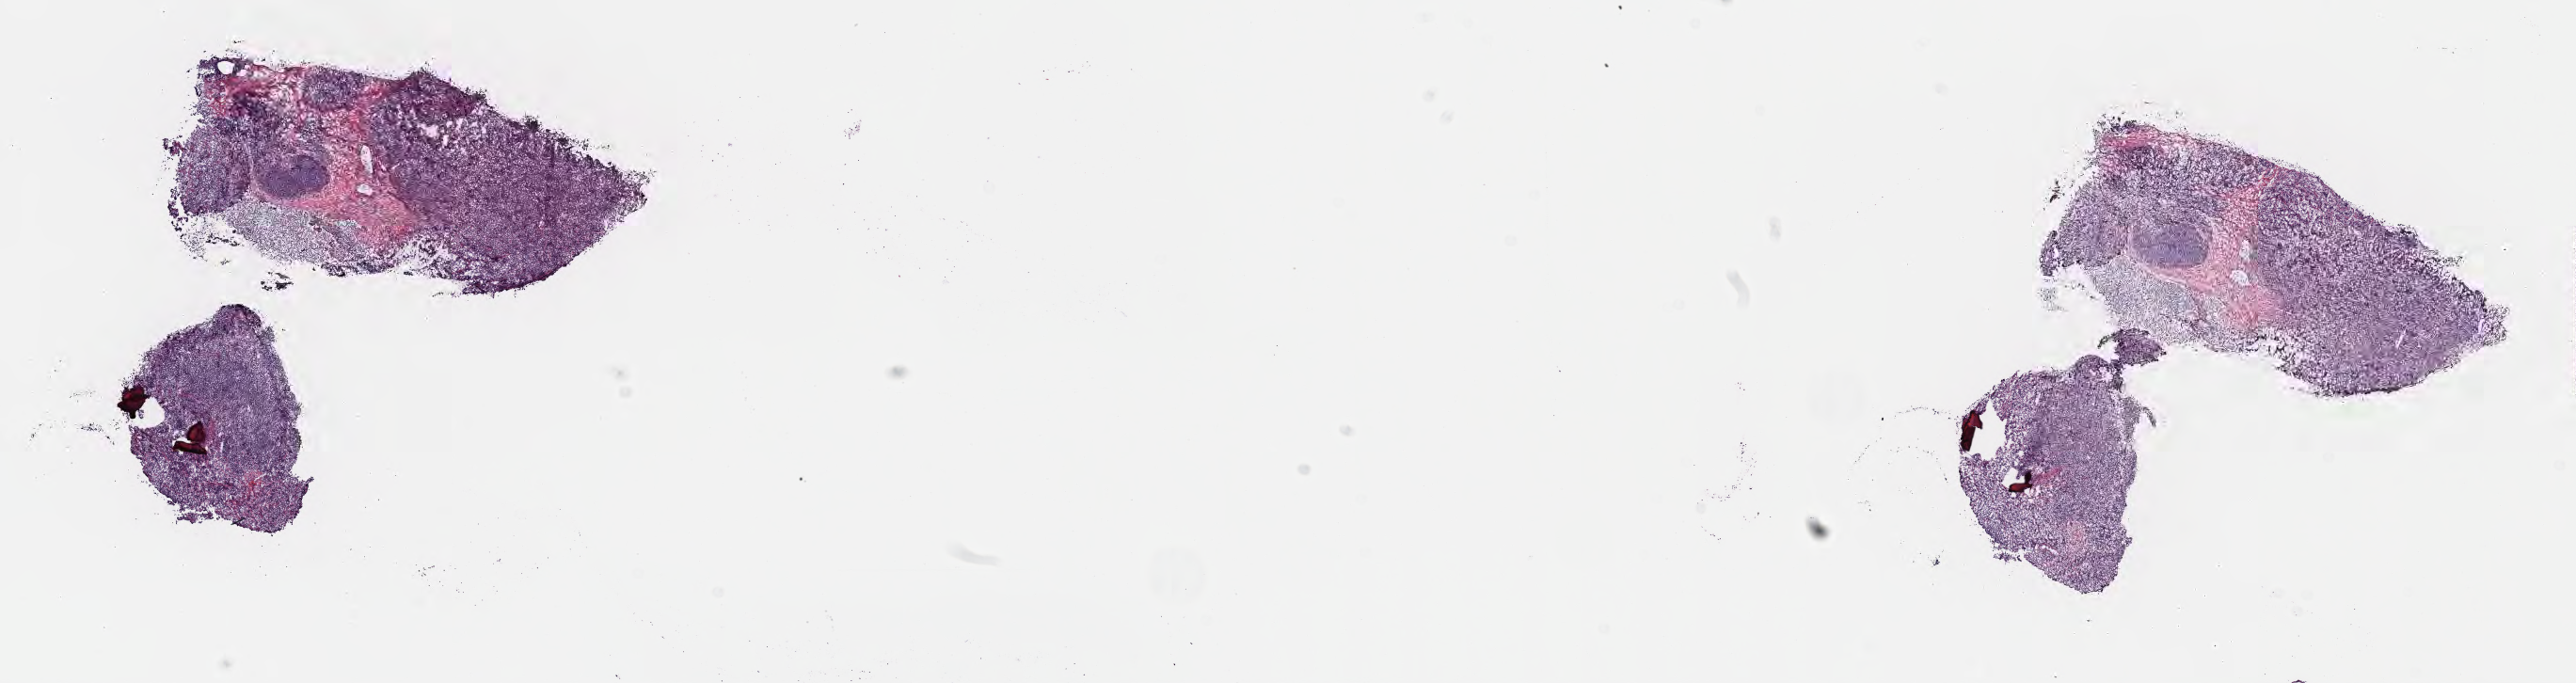
Digitized haematoxylin and eosin-stained section — whole scanned area (about 22.1 x 5.9 mm) shown as a low-resolution overview; frozen section; primary tumor; site: mandible. Patient: female, aged 13. Slide review estimates, as recorded: tumor cells 80%, tumor nuclei 90%, stromal cells 15%, necrosis 5%, normal cells 0%. Inflammatory infiltration, as recorded: lymphocyte infiltration 60%, monocyte infiltration 20%, neutrophil infiltration 5%.
Section: bottom of the tissue portion. Histologic diagnosis: Burkitt lymphoma, NOS. Ann Arbor stage (patient): Stage III.